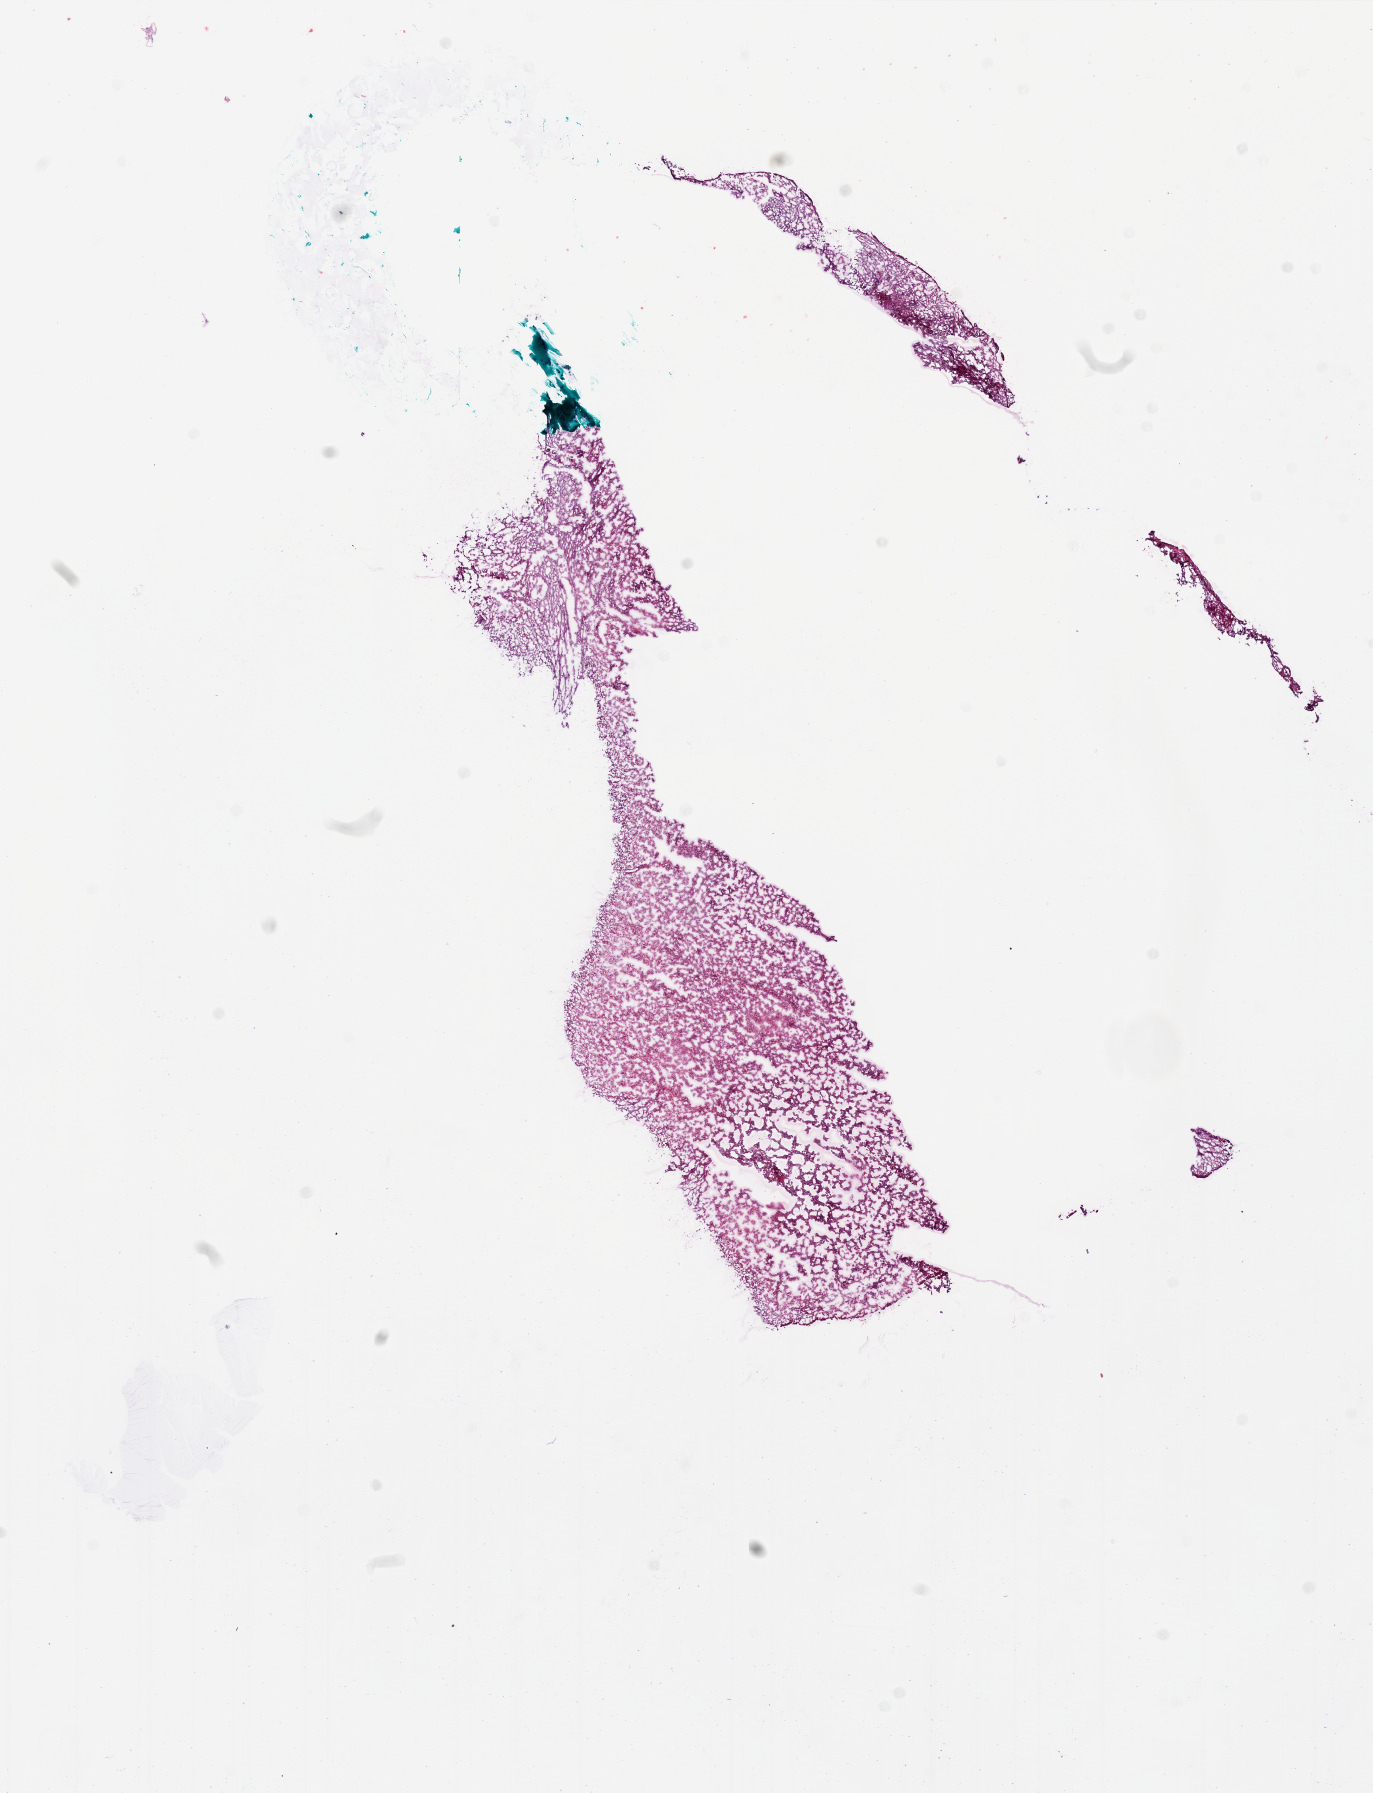
Hematoxylin and eosin (H&E) stained whole-slide image — low-resolution overview of the scanned area, about 11.0 x 14.4 mm. Slide review estimates, as recorded: tumour cells 95%, tumour nuclei 85%, normal cells 0%, stromal cells 0%, necrosis 5%.
Specimen: frozen section from the bottom of the tissue portion; brain, primary tumour sample.